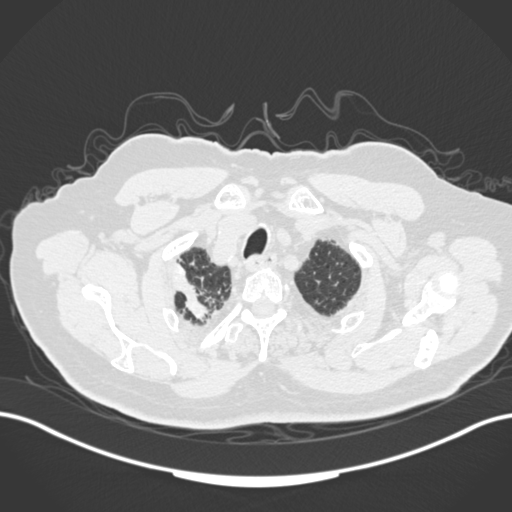
Chest CT, one axial slice. Slice 155 of 205 in the series (ordered by position). Reconstruction kernel B30f. Lung window (W 1500 / L -600 HU). 512 × 512 image matrix. Patient: male, 72 years. Case-level facts recorded for this patient, not image findings: clinical TNM (as recorded): T1a N0 M0.
Annotated regions visible in this slice (bounding box drawn by a radiologist):
- lung tumour (recorded histology: squamous cell carcinoma): bounding box (x1, y1, x2, y2) in pixels: (171, 264, 208, 322)